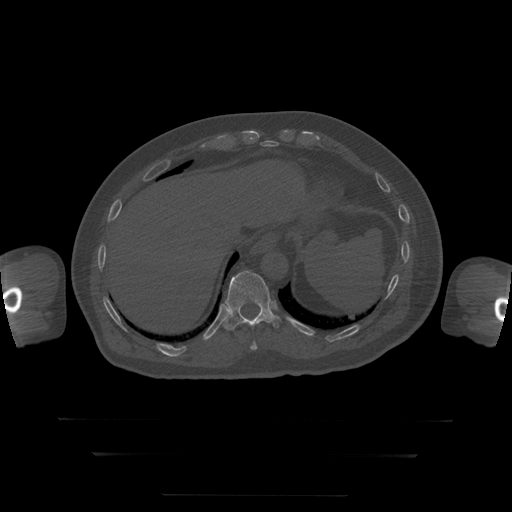
CT including the spine, one axial slice. Position 104 of 397 along the scan axis. Reconstruction kernel STANDARD. Bone window (W 1800 / L 400 HU). 1.25 mm slice thickness. 512 × 512 image matrix. Patient age 73 years. From the clinical record (not read from this slice): primary cancer: prostate.
Annotated regions visible in this slice (semi-automatic segmentation, software-assisted and operator-edited):
- T10 vertebra: bounding box [x1, y1, x2, y2] px = [251, 341, 258, 351]
- T11 vertebra: [224, 271, 281, 330]